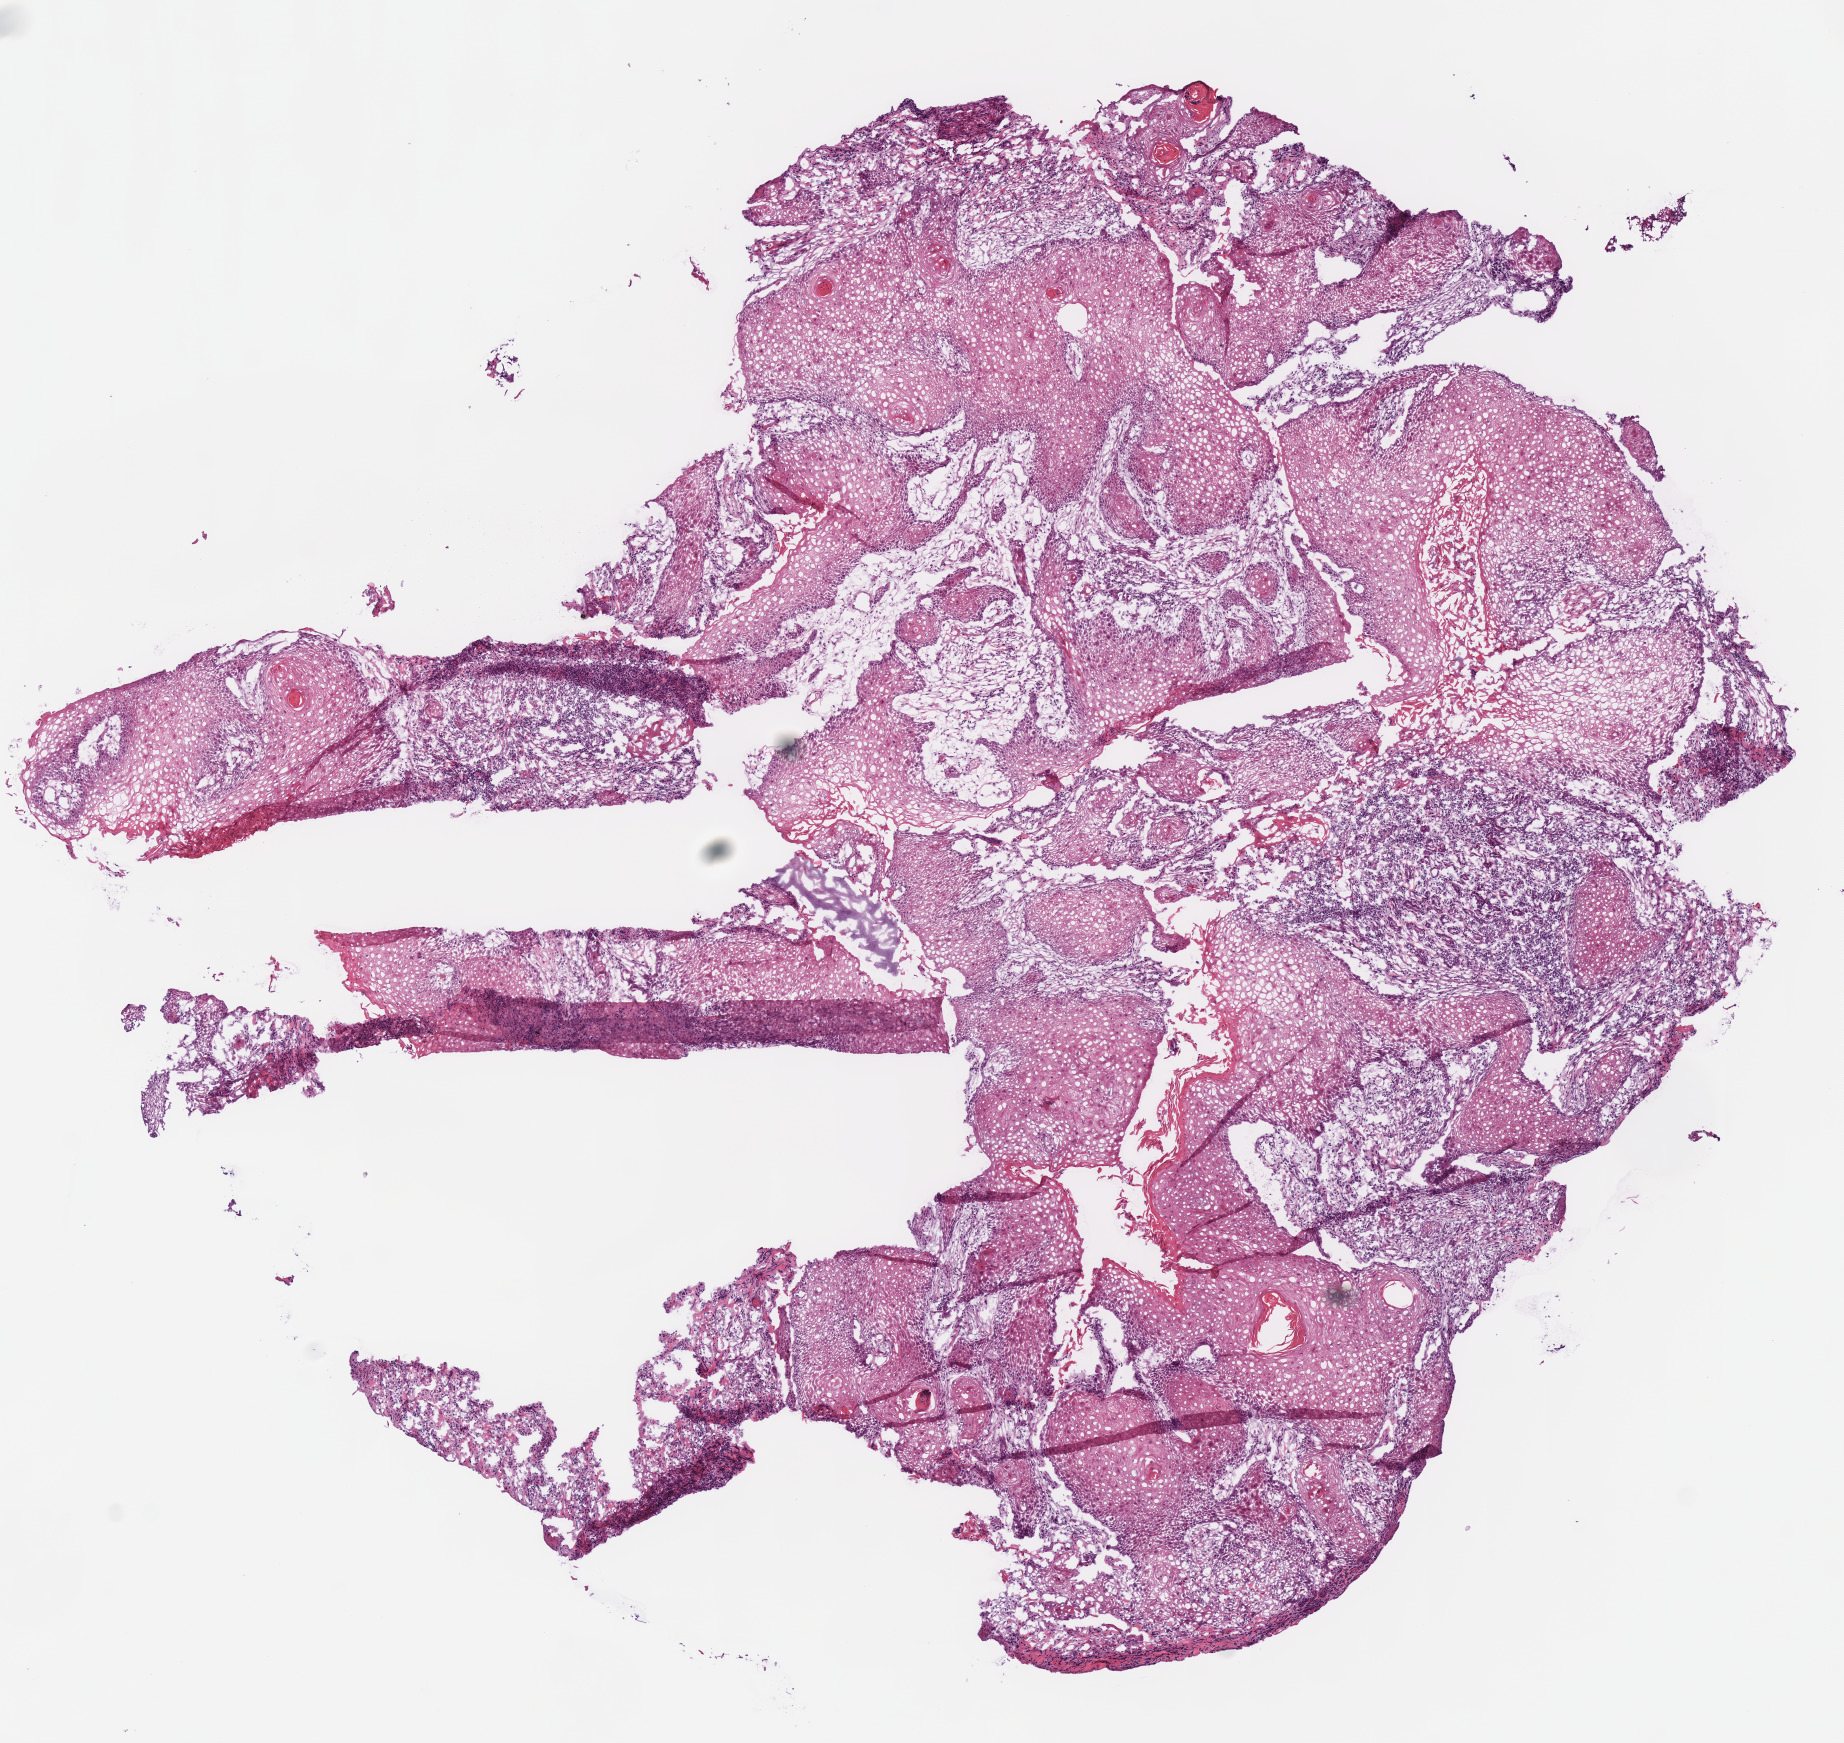
H&E whole-slide image — shown as a low-resolution overview of the whole scanned area (about 7.3 x 6.9 mm); frozen section from the bottom of the tissue portion; sample: primary tumour, head and neck. Patient: female, age at initial diagnosis 64 years. Pathologist review of this section (percent, as recorded): tumour cells 87%, tumour nuclei 75%.
Histologic diagnosis: Squamous cell carcinoma, NOS (overlapping lesion of lip, oral cavity and pharynx).